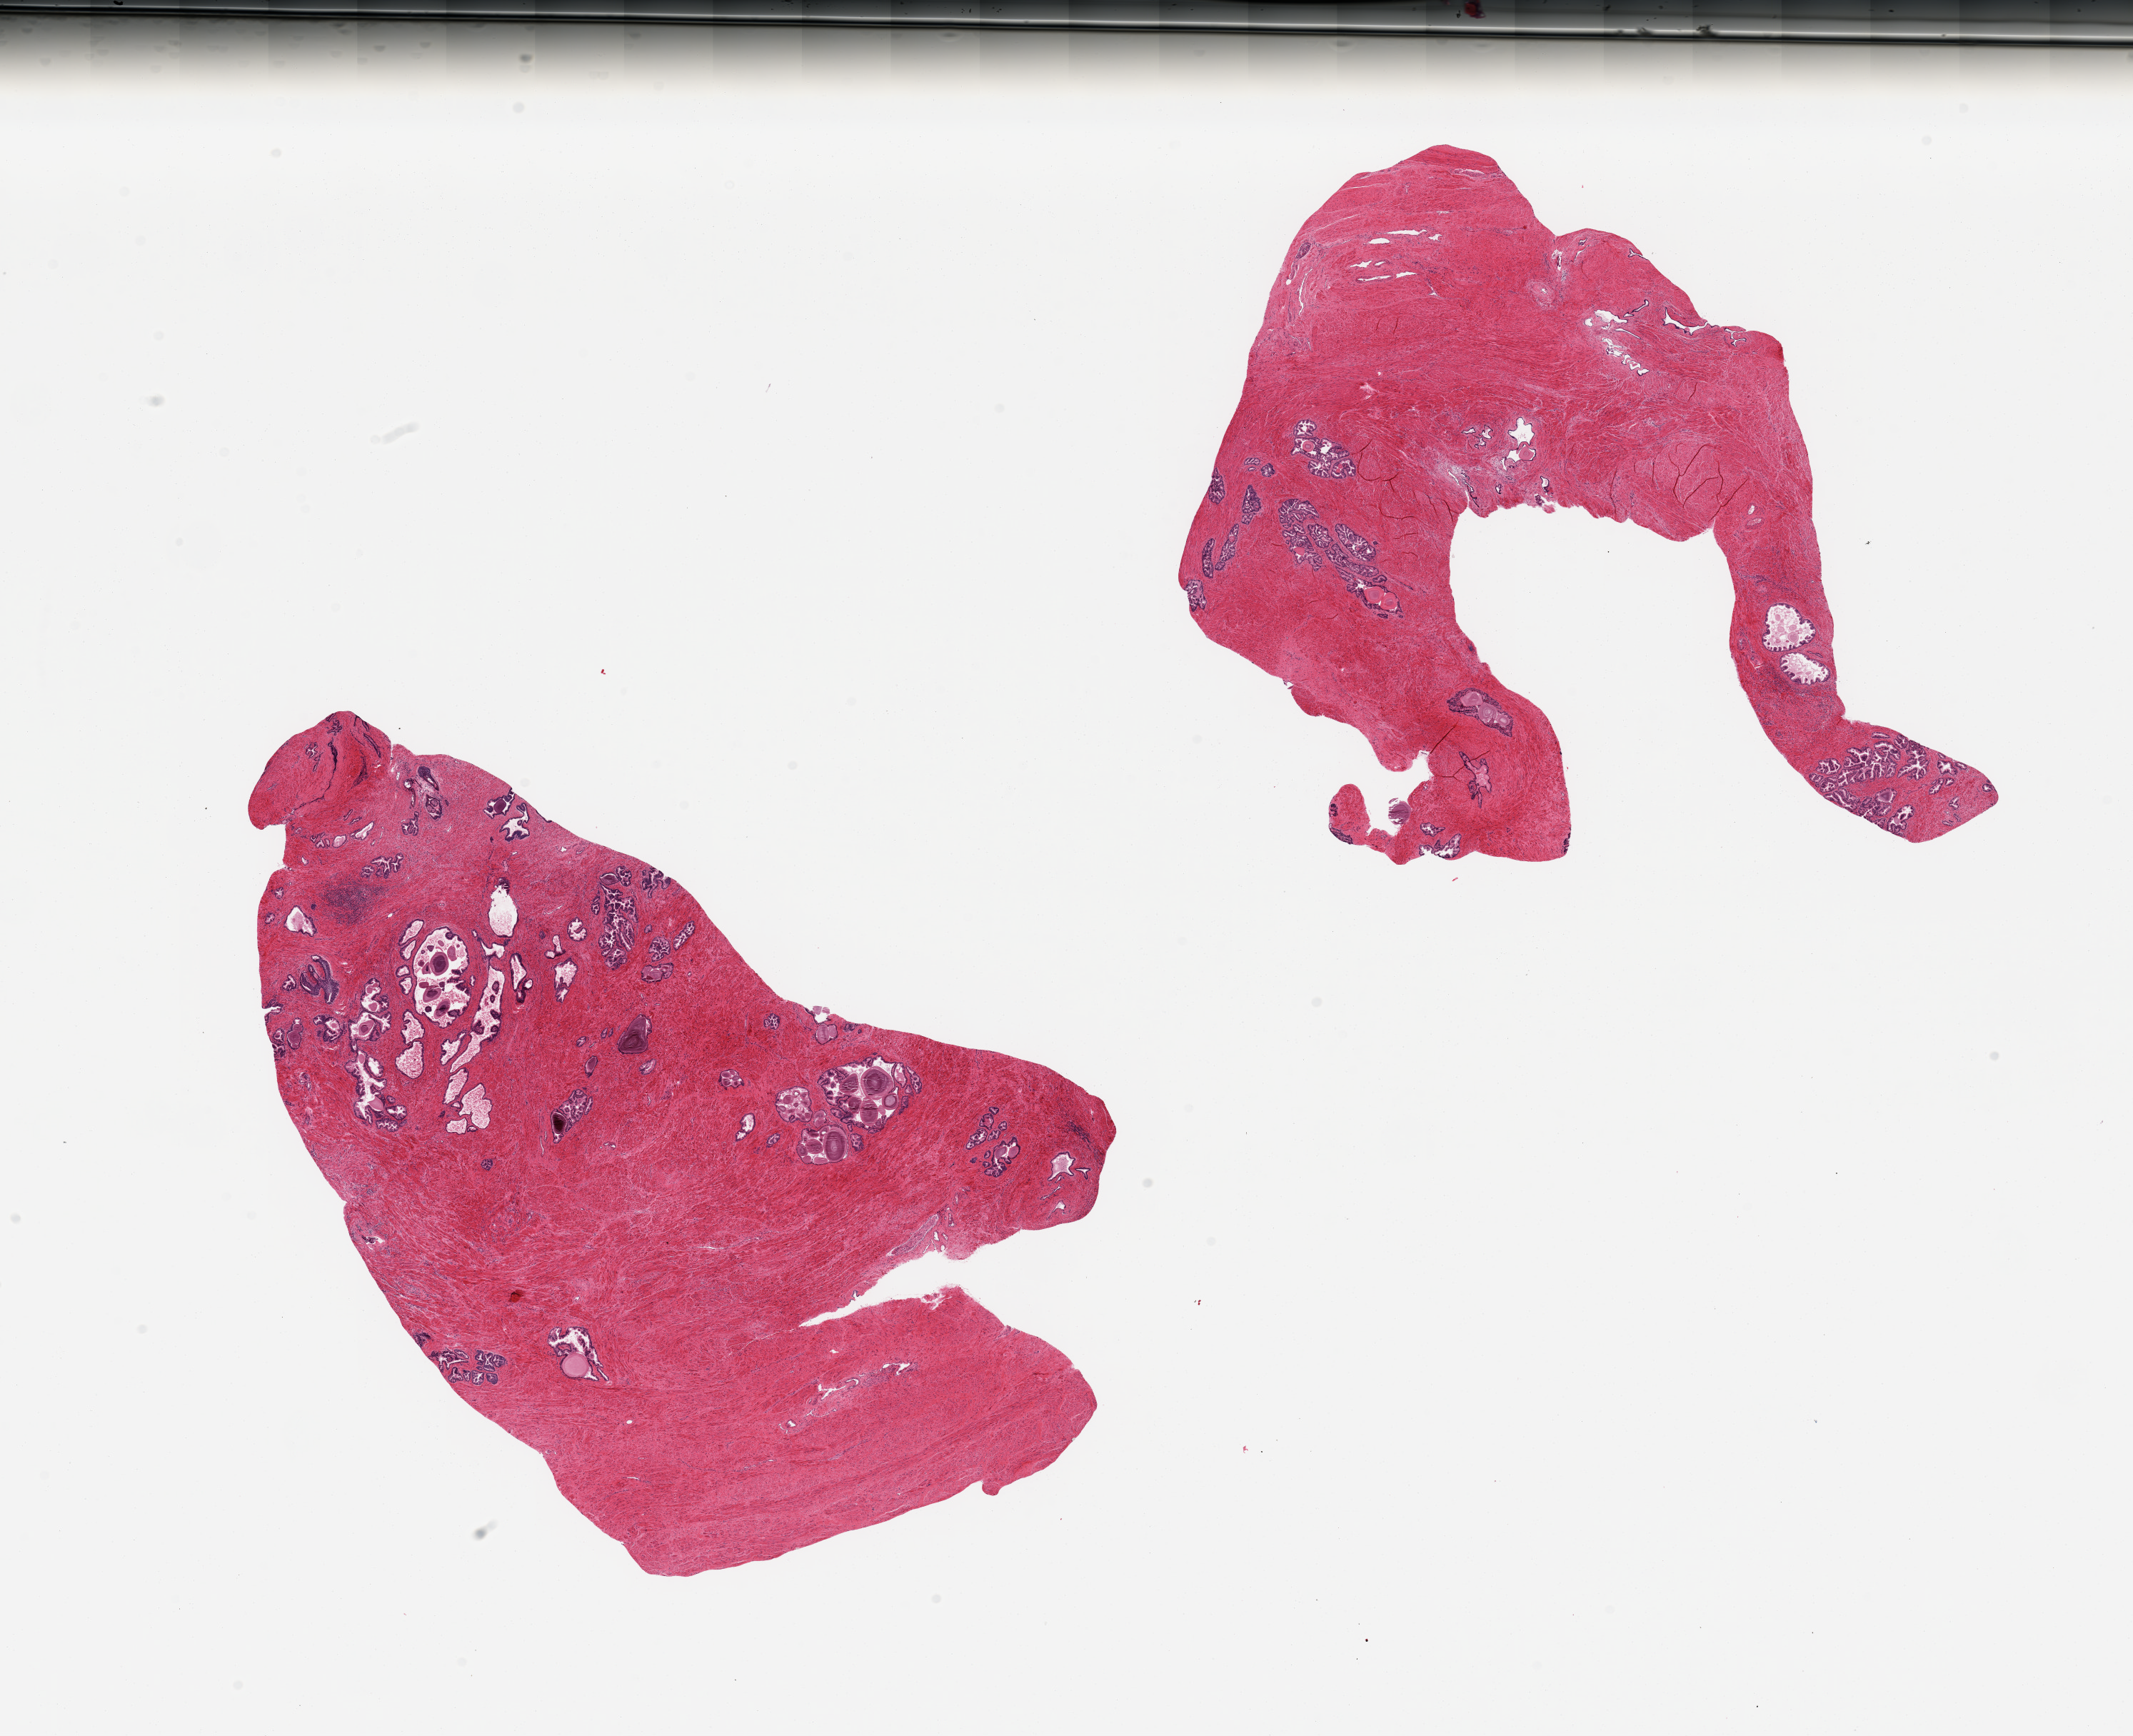
Haematoxylin and eosin whole-slide image, brightfield, a low-resolution overview of the entire scanned area, about 23.6 x 19.2 mm, PAXgene-fixed, paraffin-embedded tissue, section of prostate (target tissue), donor tissue sample. Donor: male.
Pathologist's review note for this sample: 2 pieces; mostly fibromuscular stroma.